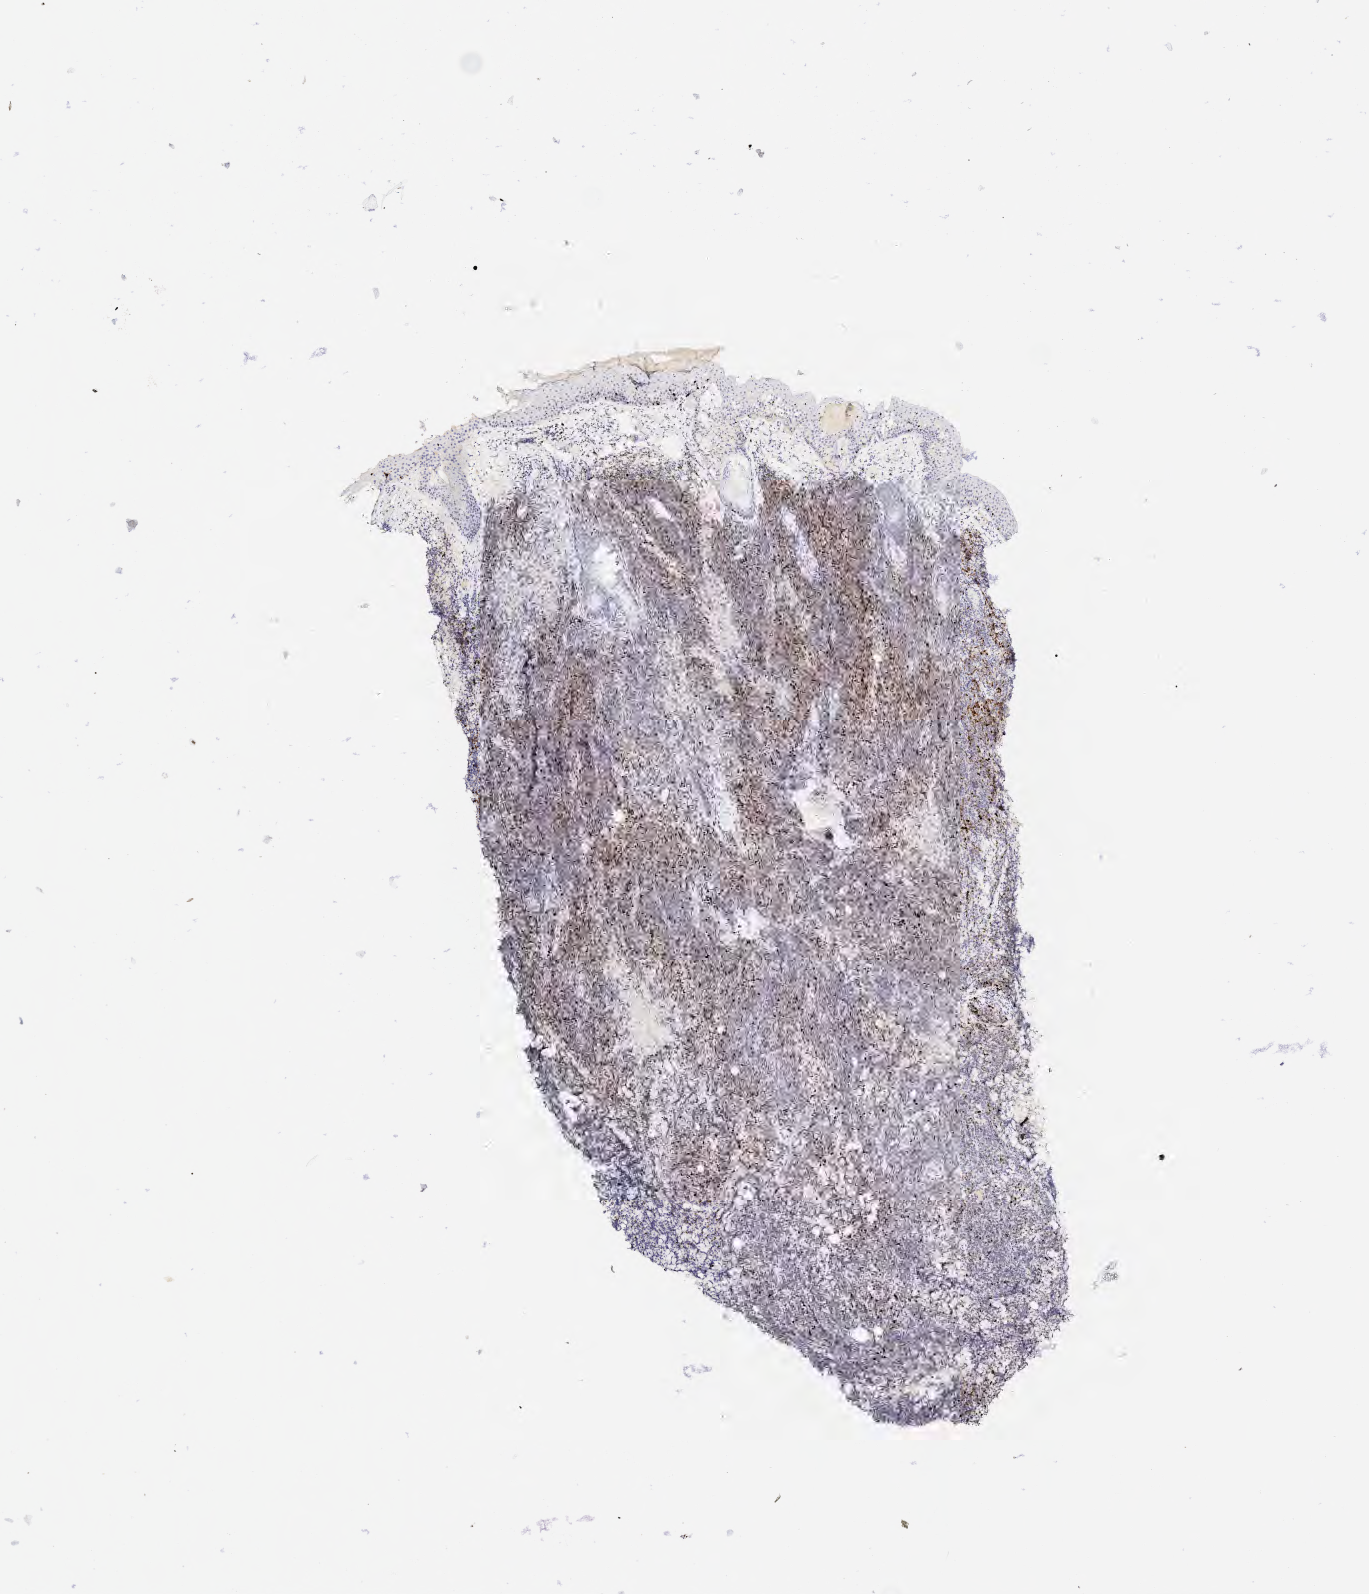
Immunohistochemistry (IHC) whole-slide image stained for IRF4/MUM1, low-resolution overview of the scanned area, about 5.5 x 6.4 mm; specimen: tumor tissue. Patient male; aged 41.
• histologic diagnosis: Diffuse large B-cell lymphoma, NOS